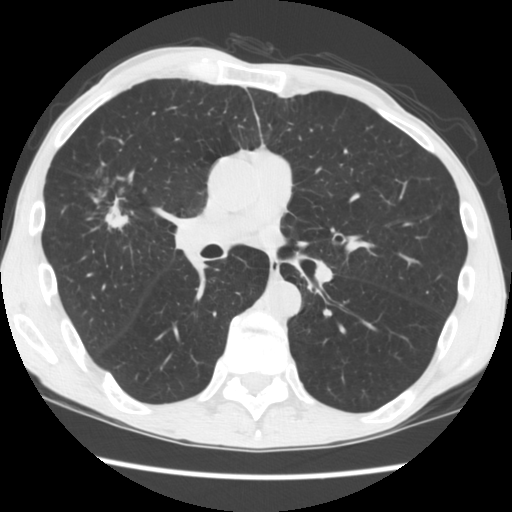
Axial slice from a low-dose chest CT screening exam; second annual screen; lung window (W 1500 / L -600 HU); standard (soft-tissue) reconstruction kernel (STANDARD); slice 87 of 181 in the series. Male, age 56 years at enrolment.
Lesion marked by an expert reader, bounding box (x1, y1, x2, y2) in pixels: (81, 156, 146, 232). The screening reader recorded 2 non-calcified nodules or masses ≥4 mm on this exam (right upper lobe, left upper lobe); which of them this box marks is not recorded. Later outcome: lung cancer diagnosed 101 days after this screen — squamous cell carcinoma, NOS, right upper lobe, right middle lobe, well differentiated (G1), stage IA (AJCC 6th edition), 27 mm at pathology.